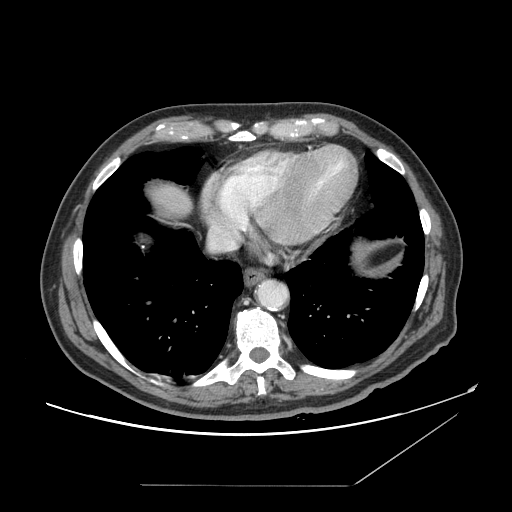
Contrast-enhanced abdominal CT, one axial slice; position 145 of 166 along the scan axis; 120 kVp; intravenous contrast given; soft-tissue window (W 400 / L 40 HU); 512 × 512 image matrix. Male patient, age 80 years. From the clinical record (not read from this slice): diagnosis: colorectal cancer liver metastases, imaged before liver resection; multiple liver metastases: no; largest metastasis: 2.2 cm; disease in both lobes: no.
Structures marked on this image (outlined manually by an expert reader):
- liver: bounding box (x1, y1, x2, y2) in pixels: (148, 185, 193, 215)
- planned liver remnant (the part of the liver to remain after resection): (147, 184, 193, 216)